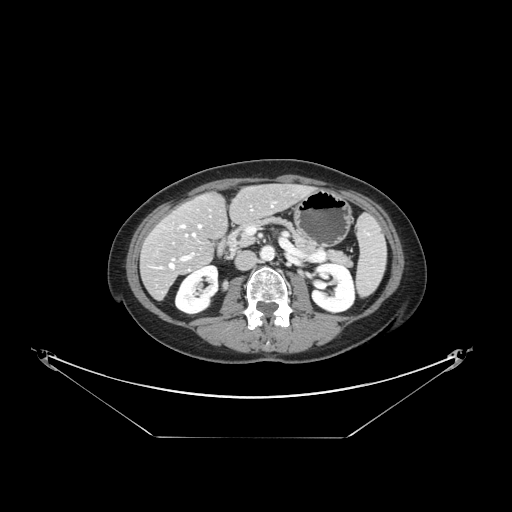
Contrast-enhanced abdominal CT, one axial slice; position 61 of 148 along the scan axis; reconstruction kernel STANDARD; intravenous contrast given; soft-tissue window (W 400 / L 40 HU); 2.5 mm slice thickness; 512 × 512 image matrix, field of view 500 × 500 mm. Female patient, age 73 years. From the clinical record (not read from this slice): diagnosis: colorectal cancer liver metastases, imaged before liver resection; multiple liver metastases: no; largest metastasis: 1 cm; disease in both lobes: no.
Outlined on this slice (manually delineated by an expert):
- hepatic veins: bounding box (x1, y1, x2, y2) in pixels: (169, 204, 273, 268)
- liver: (142, 185, 310, 298)
- planned liver remnant (the part of the liver to remain after resection): (166, 185, 309, 250)
- portal vein (with intrahepatic branches): (182, 235, 193, 260)